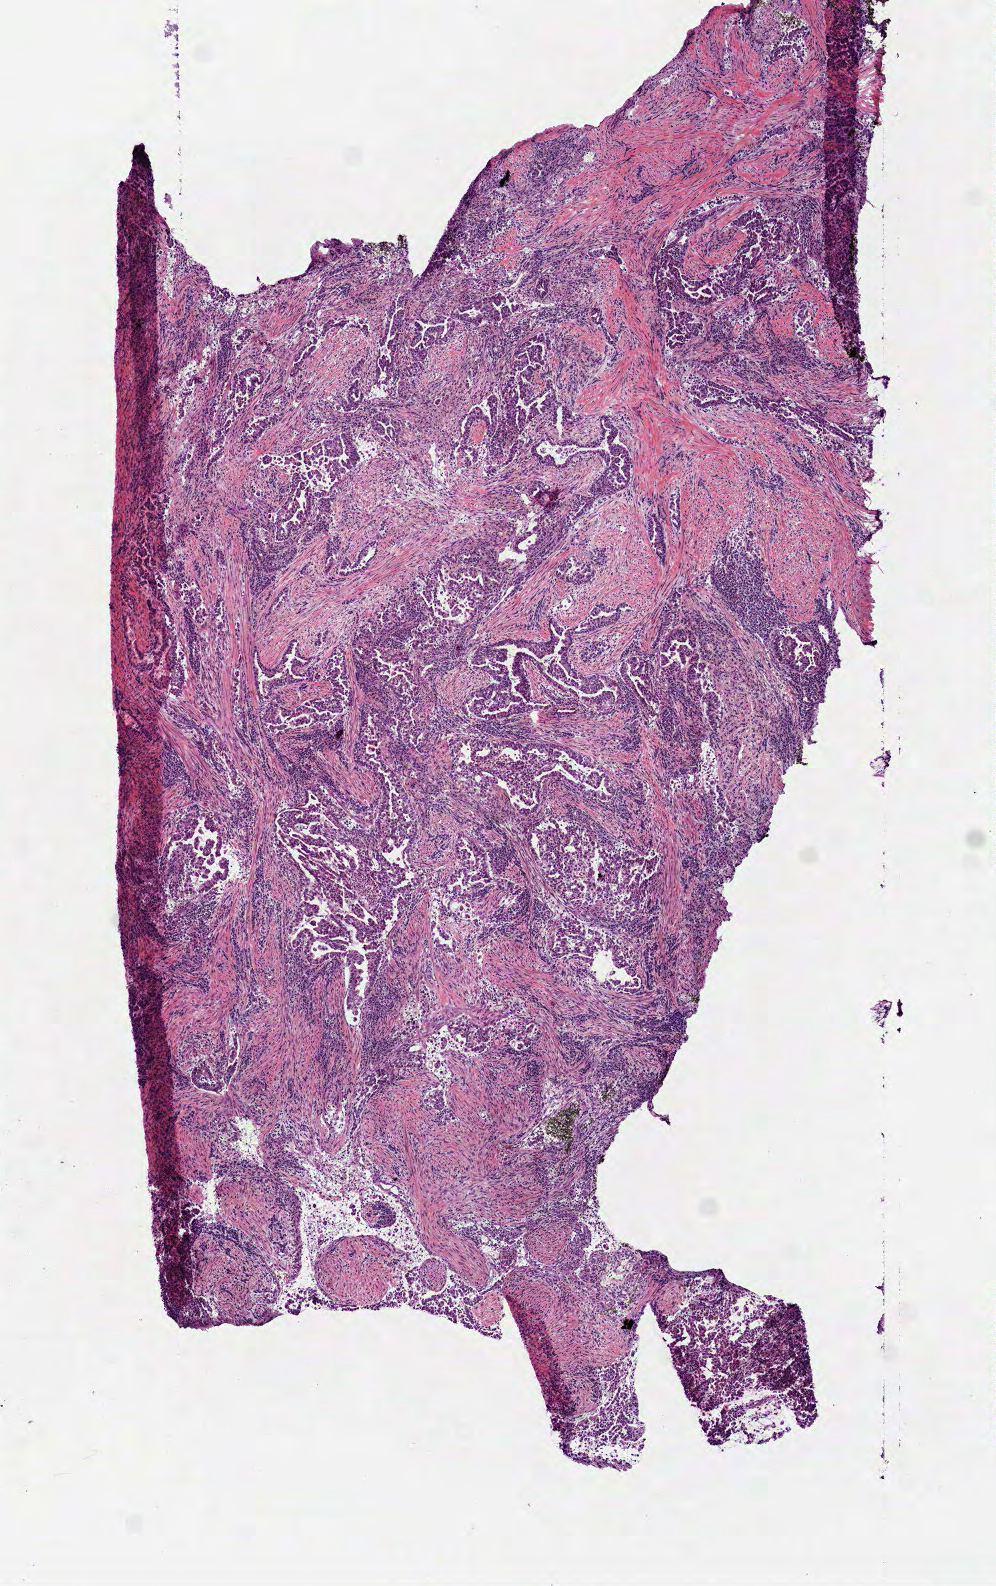
Whole-slide histology image, H&E-stained — a low-resolution overview of the entire scanned area, about 4.0 x 6.4 mm (slide scanned at 40x). Frozen section from the top of the tissue portion. Primary tumour sample from the lung. Male, age 63 years at initial diagnosis. Pathologist review of this section (percent, as recorded): tumour cells 75%, tumour nuclei 80%, normal cells 0%, stromal cells 25%, necrosis 0%.
AJCC pathologic stage: IB. Laterality: right. Diagnosis: Adenocarcinoma, NOS (lower lobe, lung). TNM: T2 N0 MX.